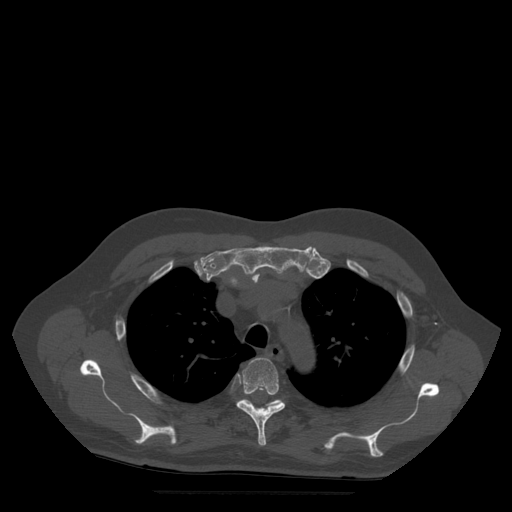
CT including the spine, one axial slice; slice 389 of 522 in the series (ordered by position); bone window (W 1800 / L 400 HU); 1.25 mm slice thickness; 512 × 512 image matrix, field of view 420 × 420 mm. Patient age 72 years. Case-level facts recorded for this patient, not image findings: primary cancer: prostate.
Annotated regions visible in this slice (semi-automatically segmented with operator editing):
- T4 vertebra: box from (x=237, y=358) to (x=286, y=446) px
- T5 vertebra: (x=241, y=400)–(x=283, y=409)